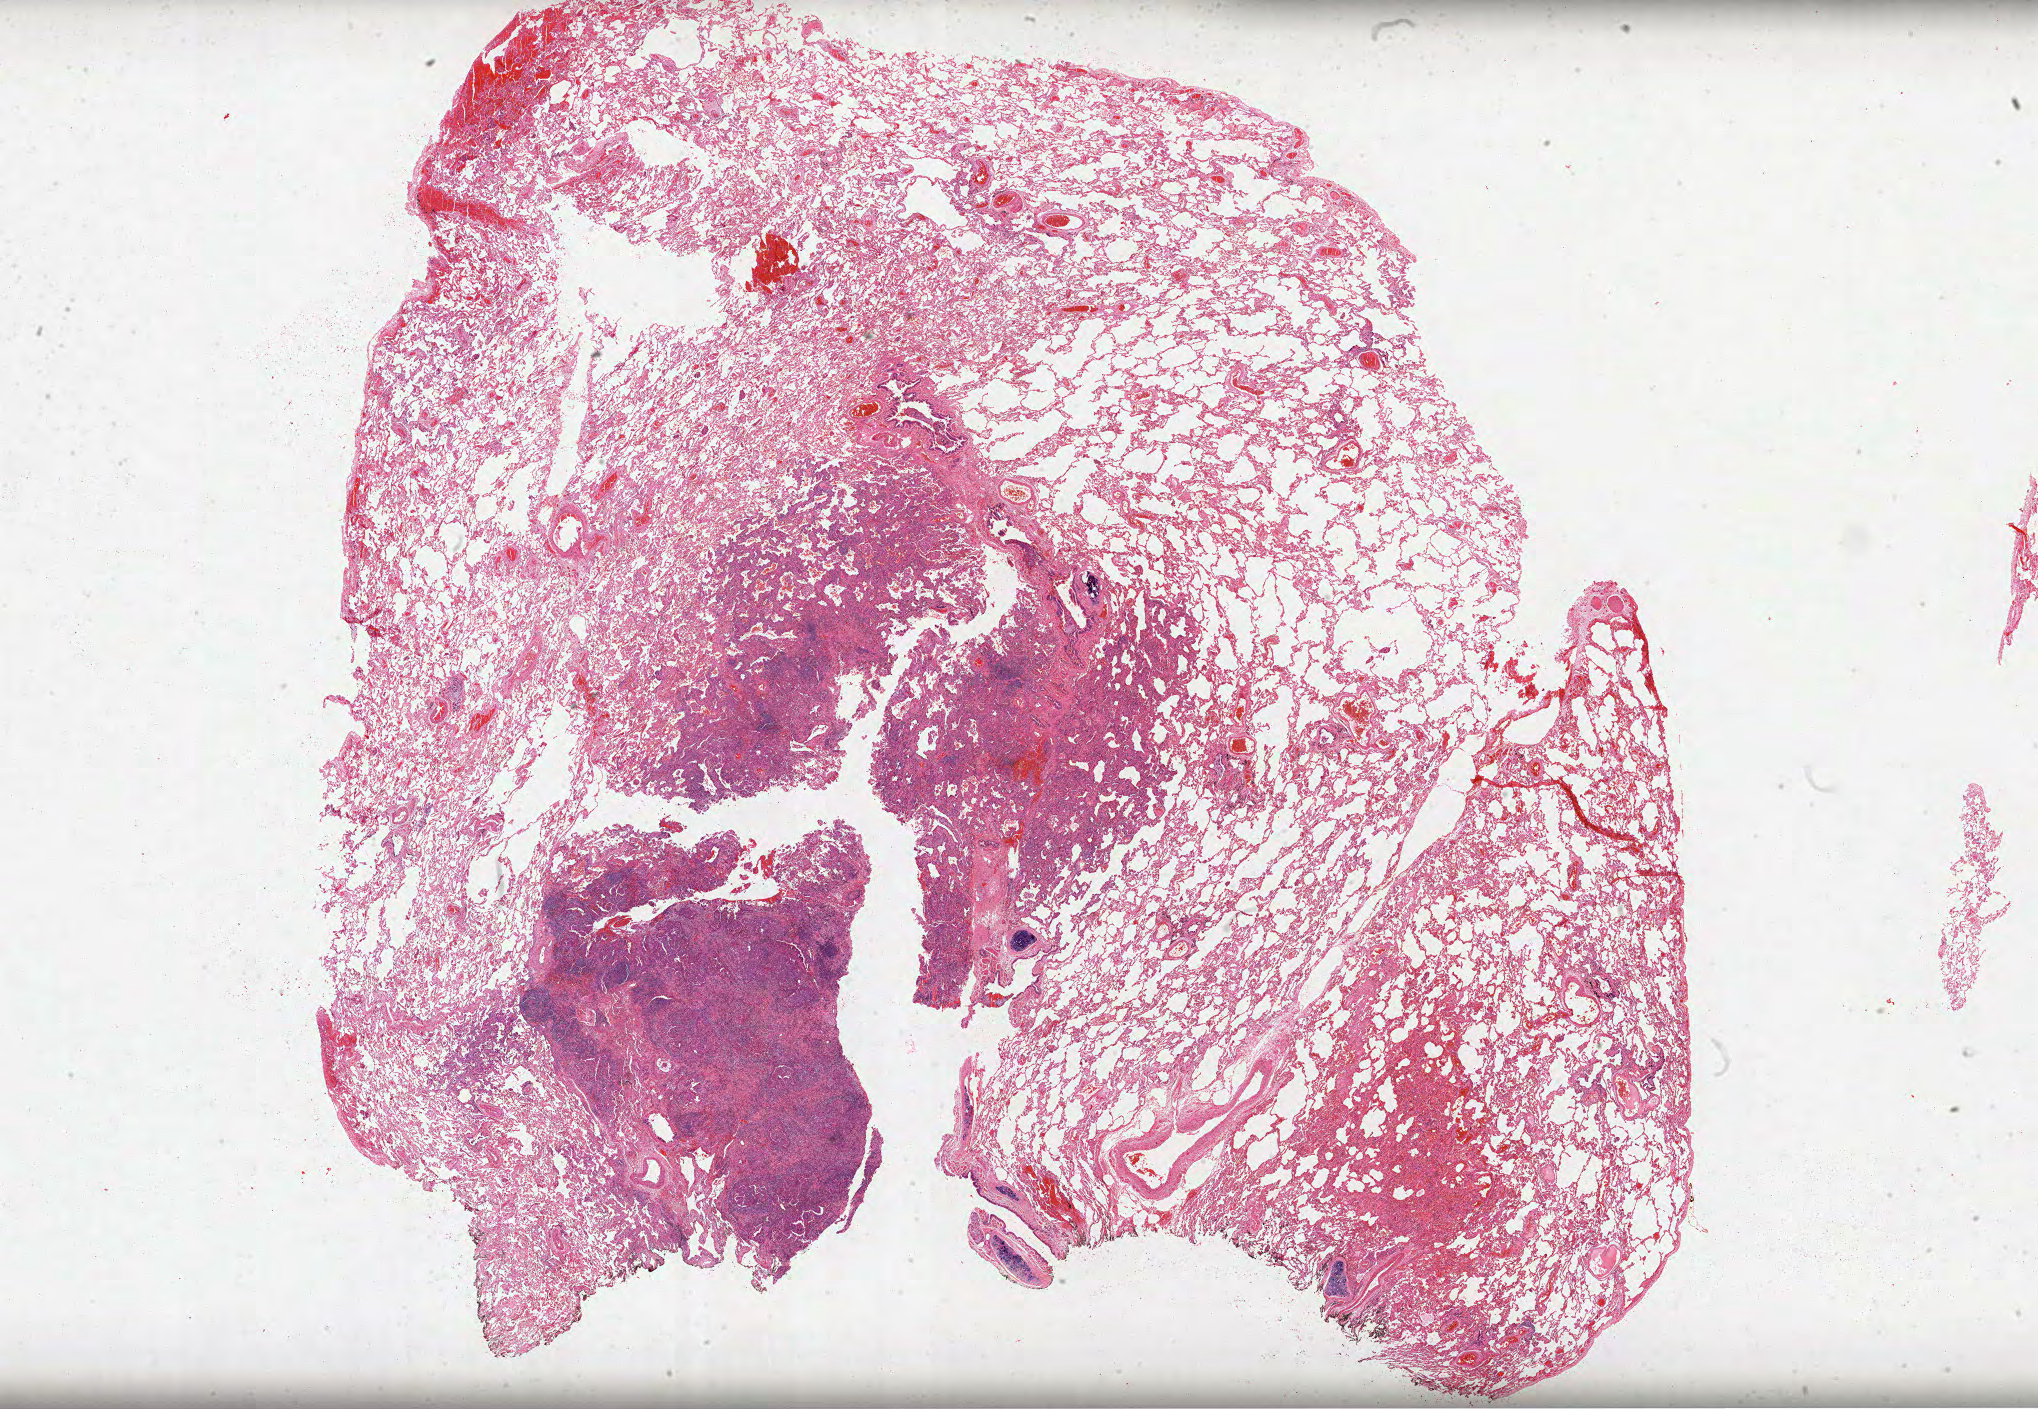
Whole-slide histology image, Hematoxylin and eosin (H&E) stained, whole scanned area (about 32.9 x 22.7 mm, slide scanned at 40x) shown as a low-resolution overview. Formalin-fixed paraffin-embedded (FFPE) diagnostic section. Primary tumour sample from the lung. Female patient; age at initial diagnosis 76 years.
* diagnosis: Adenocarcinoma with mixed subtypes (upper lobe, lung)
* AJCC pathologic stage: IA (7th edition)